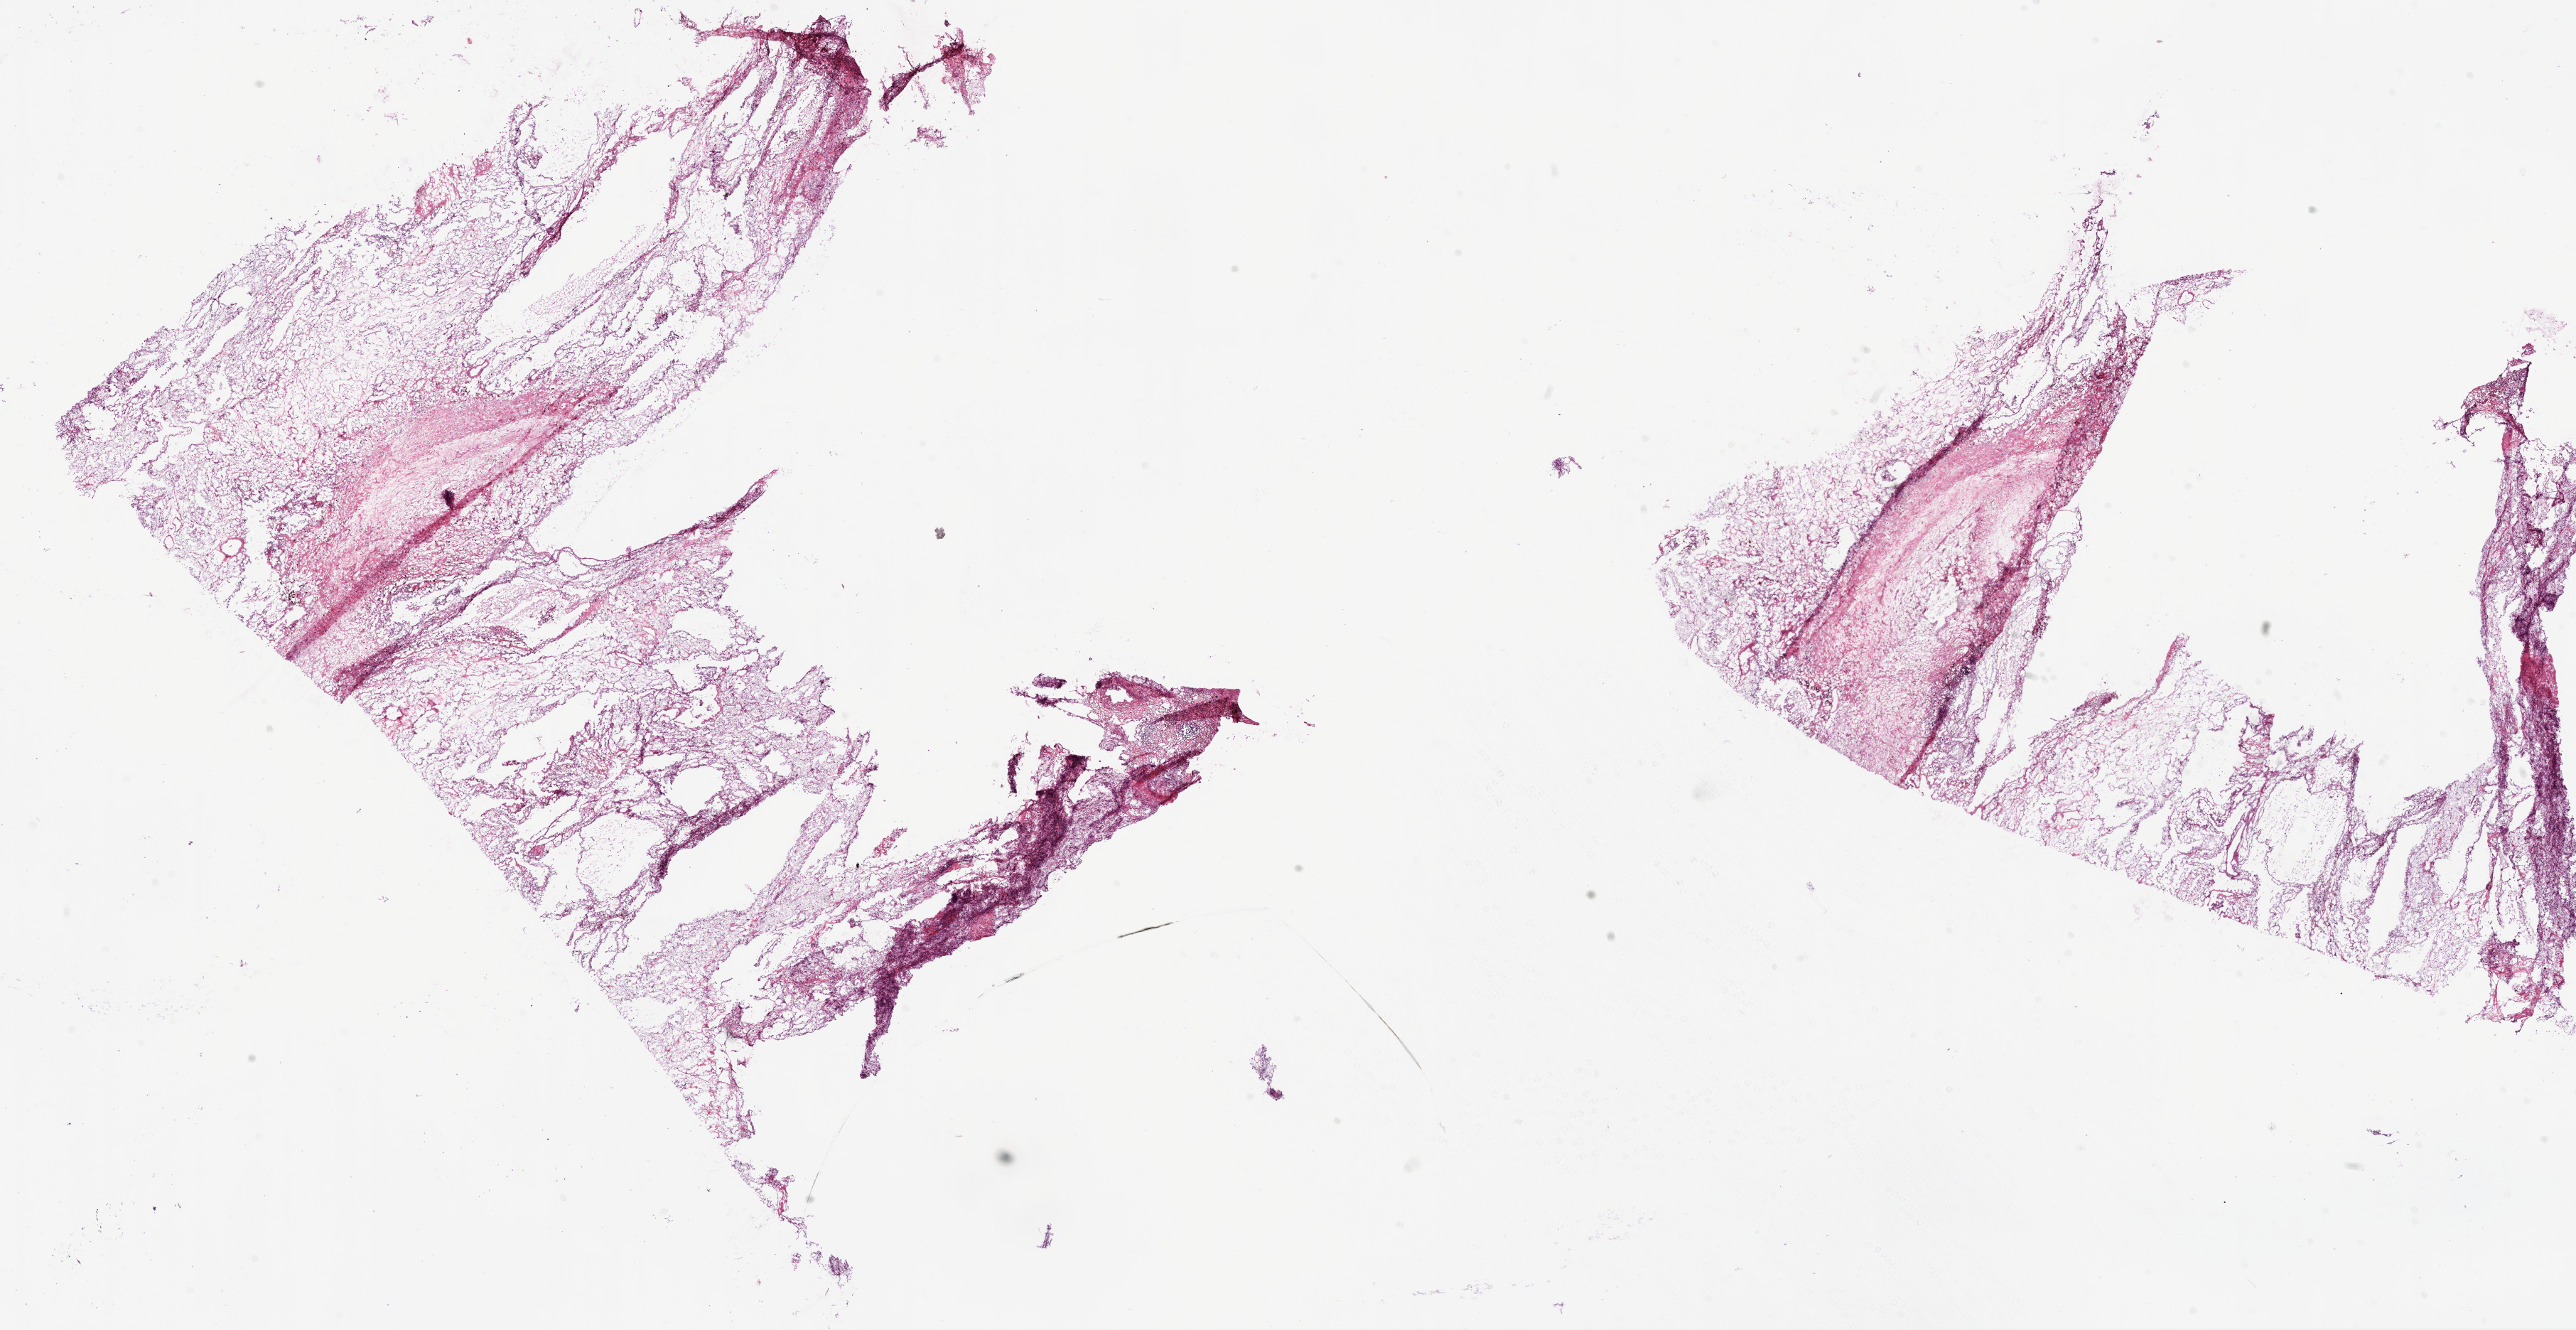
Digitized H&E-stained tissue section (whole slide) — a low-resolution overview of the entire scanned area, about 29.1 x 15.0 mm (acquisition: 20x scan). Frozen section. Sample: primary tumour, kidney. Male patient; age at initial diagnosis 88 years. Histologic grade: G2 (moderately differentiated). Composition of this section per pathologist review: tumour cells 80%, tumour nuclei 85%, normal cells 0%, stromal cells 20%, necrosis 0%.
* TNM: T1a N0 M0
* laterality: right
* AJCC pathologic stage: I
* diagnosis: Clear cell adenocarcinoma, NOS